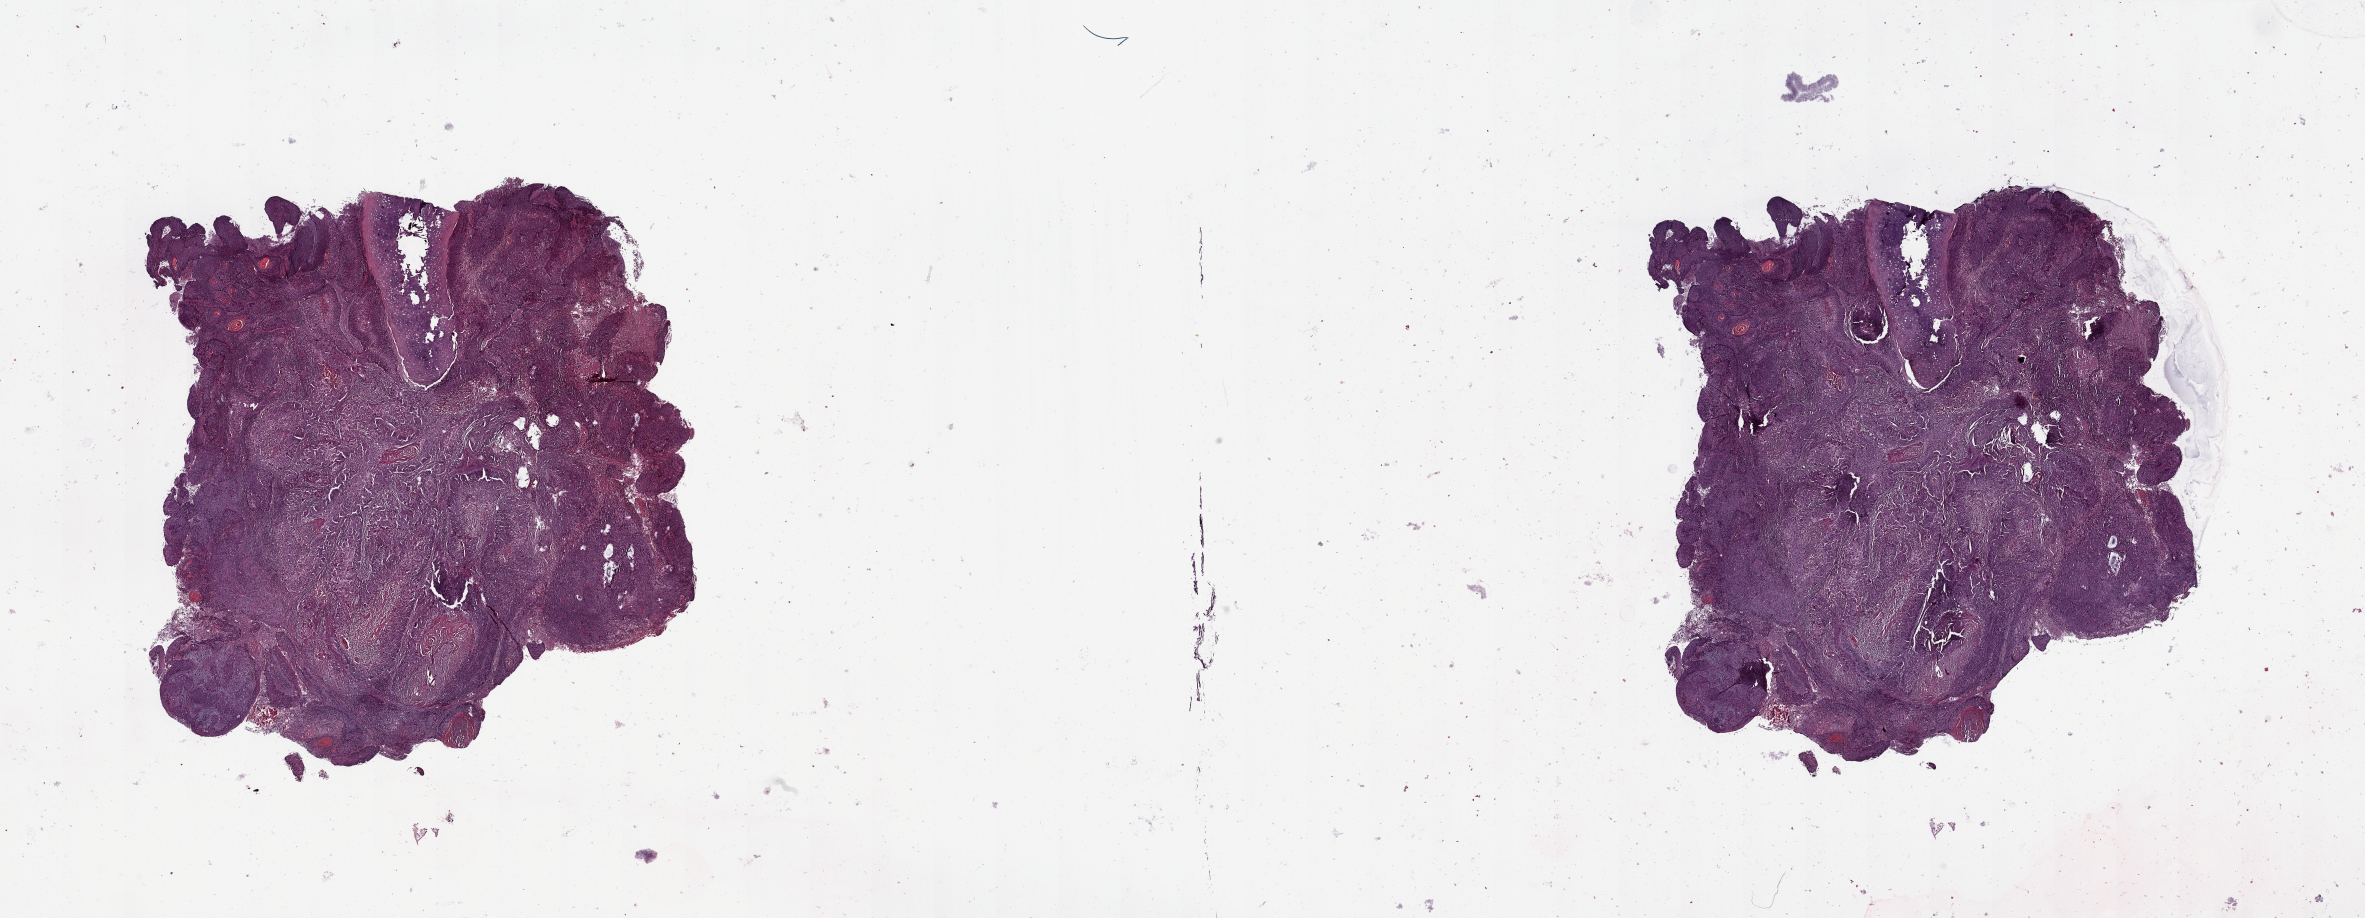
Hematoxylin and eosin (H&E) stained whole-slide image, whole scanned area (about 37.4 x 14.5 mm) shown as a low-resolution overview, tumour tissue sample, sampled site: lung. Male, 66 y/o. Histologic grade: G2 (moderately differentiated). Pathologist review of this section (percent, as recorded): tumour nuclei 80%, necrosis 5%.
• diagnosis: Squamous cell carcinoma, NOS
• primary tumour site (as recorded): left upper lobe
• AJCC pathologic stage: IIA